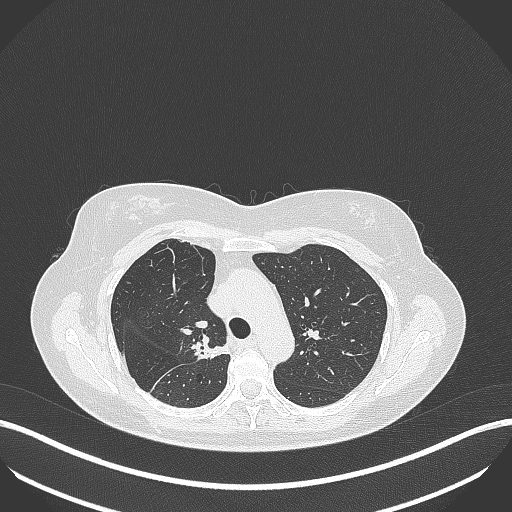
Chest CT, one axial slice. Position 278 of 386 along the scan axis. 120 kVp. Lung window (W 1500 / L -600 HU). 1 mm slice thickness. 512 × 512 image matrix. Patient: female, 65 years. Case-level facts recorded for this patient, not image findings: clinical TNM (as recorded): T1b N0 M0; histopathological grade: G2.
Outlined on this slice (bounding box drawn by a radiologist):
- lung tumour (recorded histology: adenocarcinoma): box from (x=190, y=338) to (x=230, y=364) px